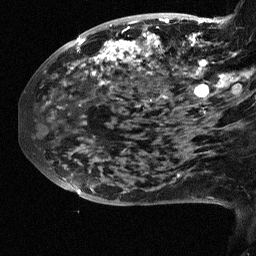
Breast MRI (dynamic contrast-enhanced), one sagittal slice; slice 24 of 64 in the series (ordered by position); dynamic contrast-enhanced study with each time point stored as its own series, time point 2 of 3 at this slice position (early post-contrast, ordered by acquisition time); 1.5 T; TE 4.5 ms, TR 11 ms; 2.5 mm slice thickness; 256 × 256 image matrix, field of view 200 × 200 mm. Female patient, age 38 years. Case-level facts recorded for this patient, not image findings: setting: breast cancer imaged before/during neoadjuvant chemotherapy; receptor status: HR-positive, HER2-negative.
Outlined on this slice (semi-automatically segmented with operator editing):
- analysis volume of interest (the breast-tissue region the enhancement analysis was run in; not a lesion): bounding box <88,18,252,126> (left, top, right, bottom; pixels)
- tumour enhancement mask (voxels above the 90 % enhancement threshold inside the analysis volume of interest): <92,19,252,112>